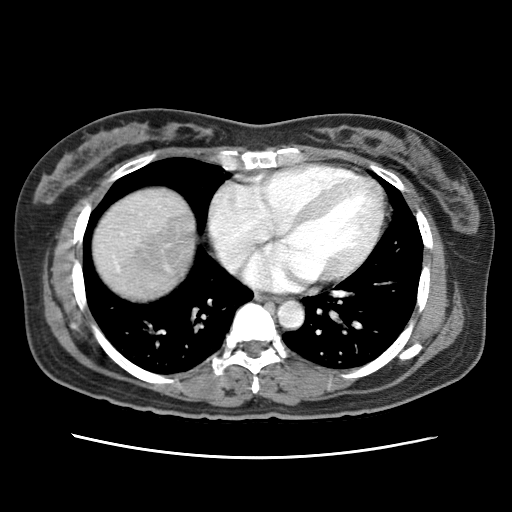
Contrast-enhanced abdominal CT (liver protocol), one axial slice. Position 68 of 79 along the scan axis. Reconstruction kernel STANDARD. Soft-tissue window (W 400 / L 40 HU). 2.5 mm slice thickness. 512 × 512 image matrix. From the clinical record (not read from this slice): diagnosis: hepatocellular carcinoma (patient treated with transarterial chemoembolisation; whether this scan precedes or follows treatment is not stated here); TNM stage (as recorded): Stage-I; Child-Pugh class: A; tumour differentiation: moderately differentiated; tumour nodularity: uninodular.
Outlined on this slice (semi-automatically segmented with operator editing):
- abdominal aorta: bounding box <277,300,303,328> (left, top, right, bottom; pixels)
- liver parenchyma outside the tumour (the mass and vessels are separate outlines, so this box may not span the whole liver): <94,190,194,298>